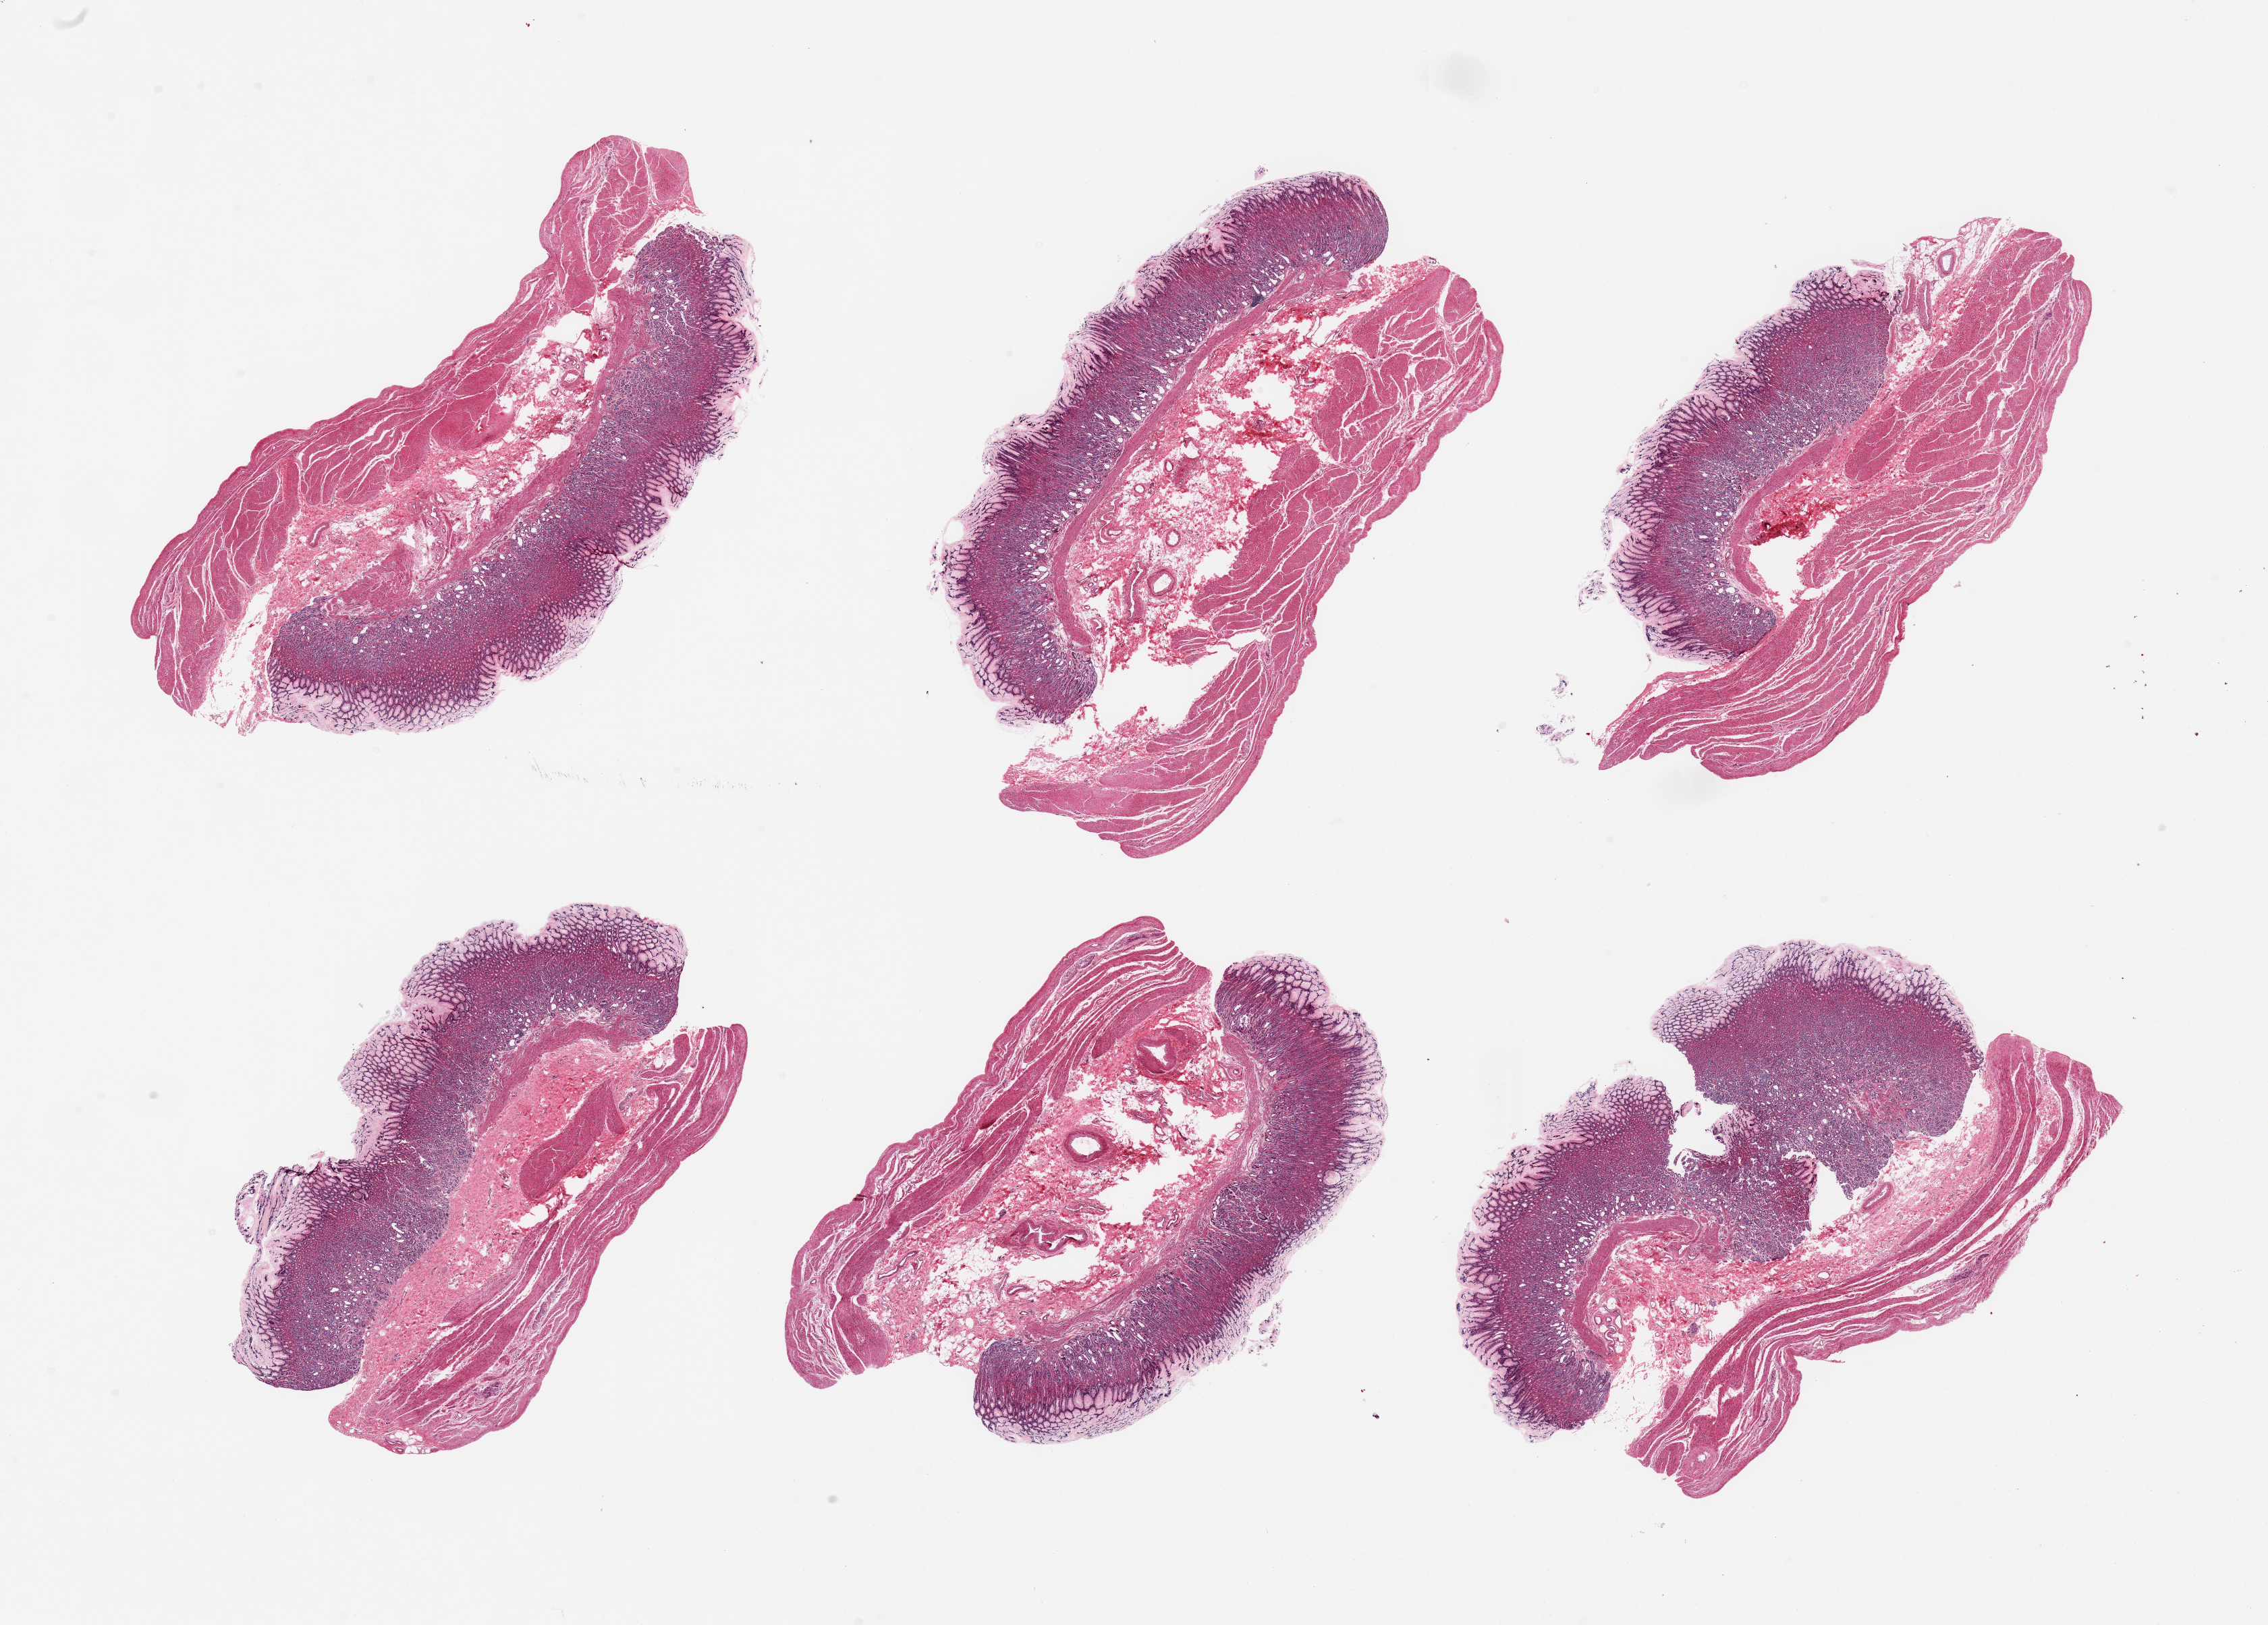
Whole-slide image, hematoxylin and eosin (H&E) stain — low-resolution overview of the scanned area, about 26.6 x 19.0 mm, PAXgene-fixed paraffin-embedded (PFPE) section, sampled site (target tissue): stomach, tissue donor sample. Donor: male.
Review note (as recorded): 6 pieces, mucosa well preserved, up to ~1mm, patchy microcystic glandular metapasia/gastropathy.